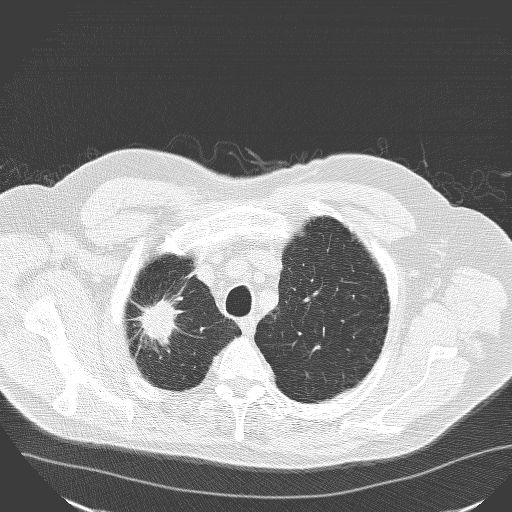
Low-dose screening chest CT, one axial slice; 120 kVp; lung window (W 1500 / L -600 HU); 3.2 mm slice thickness; 512 × 512 image matrix, field of view 400 × 400 mm.
Structures marked on this image (manually delineated by an expert):
- lesion 1 (tumor, upper lobe of right lung): bounding box <141,298,176,340> (left, top, right, bottom; pixels)